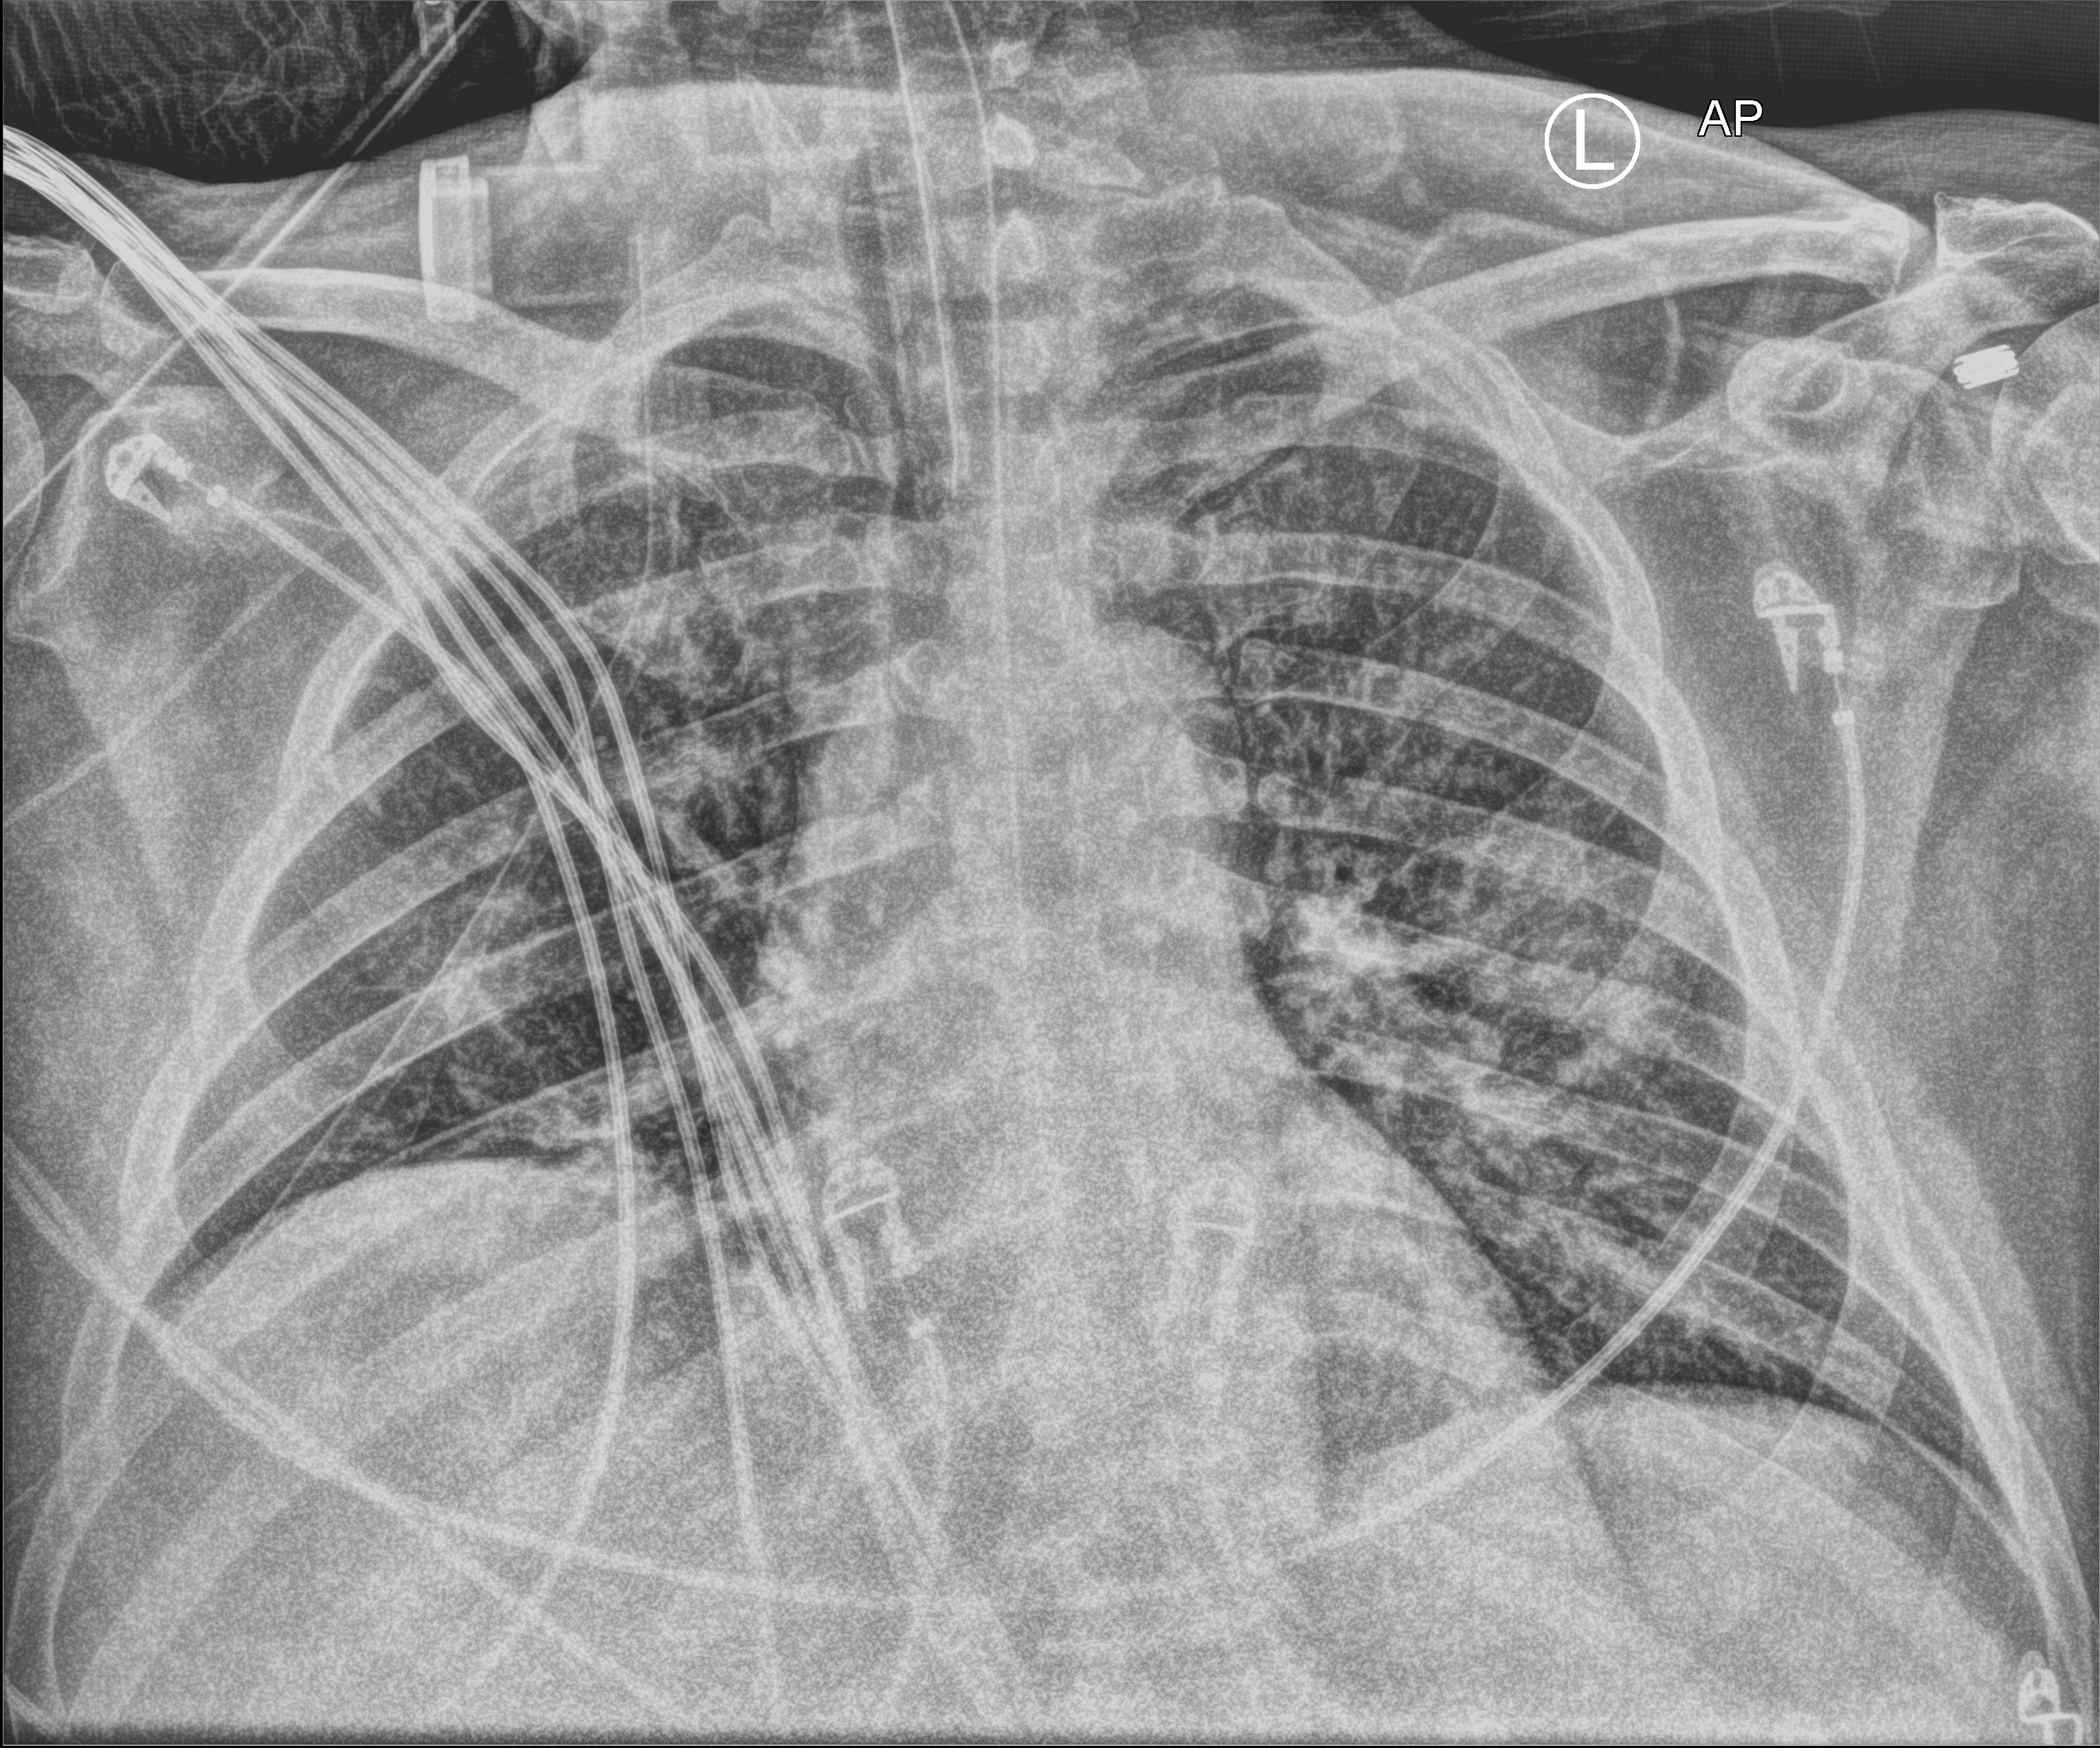
Chest X-ray (portable). Male patient hospitalised with COVID-19, age 18–59 years.
Admission-level facts for this patient (not findings on this image; timing relative to this image not recorded): COPD (admission record): no; length of hospital stay: 28 days; diabetes (admission record): yes.